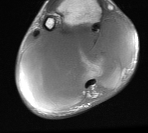
MRI of an extremity soft-tissue mass, one axial slice; slice 19 of 76 in the series (ordered by position); MR volume resampled by the dataset authors to the PET/CT grid (not the native acquisition matrix); 3.27 mm slice thickness; 148 × 133 image matrix. Male patient. From the clinical record (not read from this slice): histological type: liposarcoma - round cell; grade: high; site of the primary tumour: right calf.
Annotated regions visible in this slice (expert contour drawn on MRI and transferred to this co-registered scan by the dataset authors):
- gross tumour volume (mass): bounding box (x1, y1, x2, y2) in pixels: (20, 16, 137, 111)